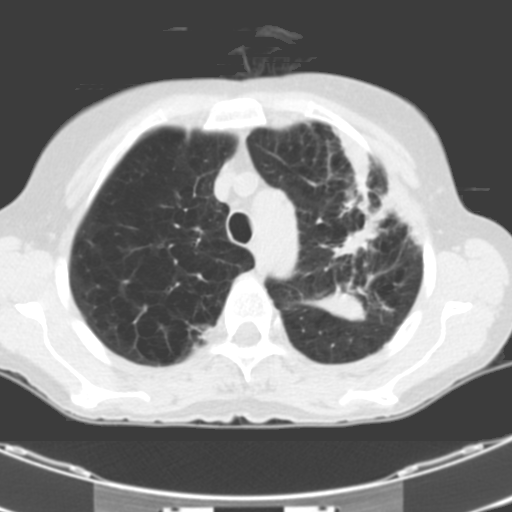
Low-dose screening chest CT, one axial slice. Slice 82 of 106 in the series (ordered by position). 120 kVp. One of 2 acquisitions stored at this slice position. Lung window (W 1500 / L -600 HU). 3.2 mm slice thickness. 512 × 512 image matrix, field of view 299 × 299 mm.
Annotated regions visible in this slice (outlined manually by an expert reader):
- lesion 1 (tumor): box from (x=319, y=290) to (x=366, y=321) px